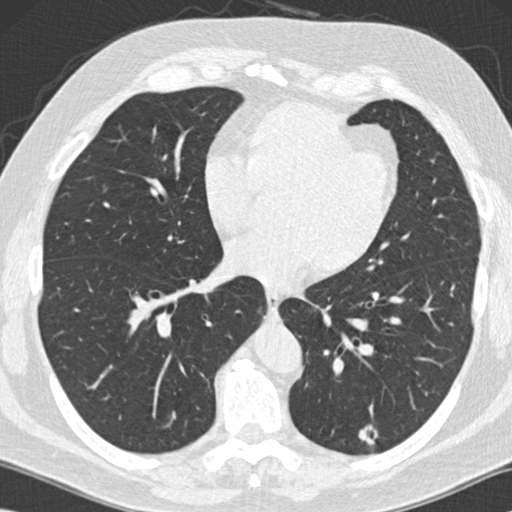
Low-dose screening chest CT, one axial slice. Position 58 of 152 along the scan axis. Reconstruction kernel B30f. 120 kVp. Lung window (W 1500 / L -600 HU). 2 mm slice thickness. 512 × 512 image matrix.
Annotated regions visible in this slice (outlined manually by an expert reader):
- lesion 1 (tumor, lower lobe of left lung): box from (x=359, y=425) to (x=378, y=445) px